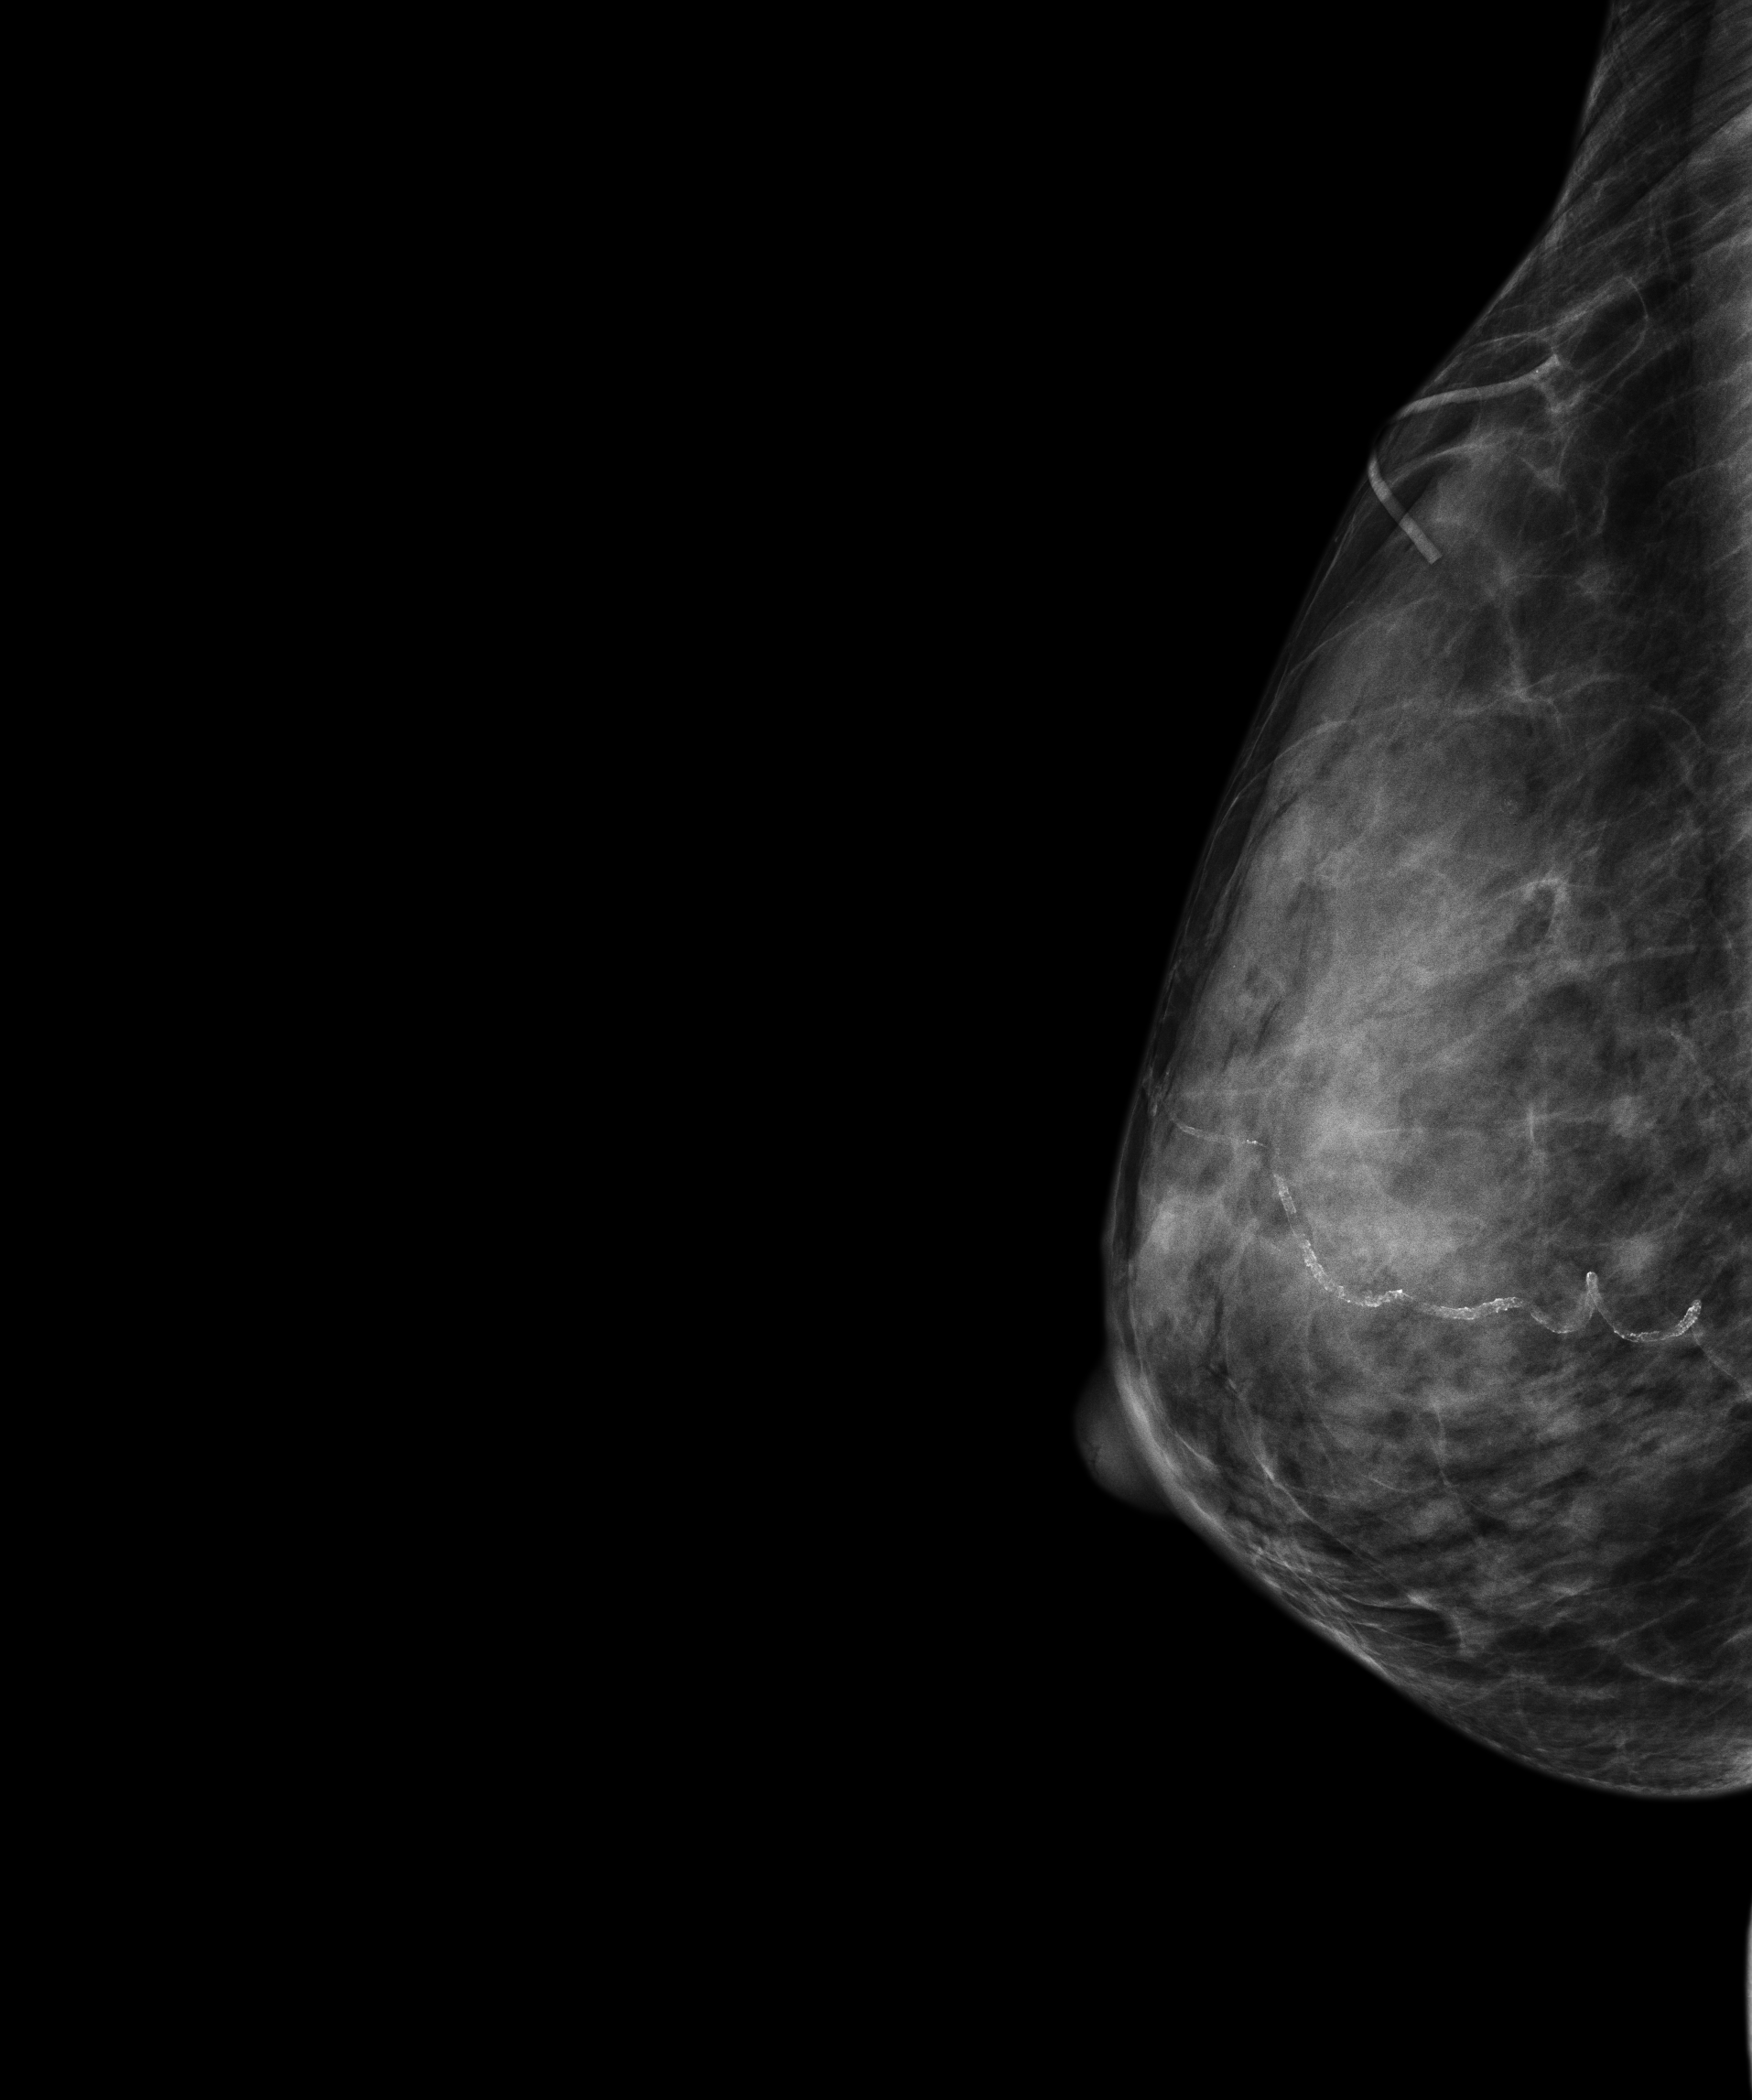
Annual screening mammography examination; compressed breast thickness 29 mm. Patient: female, 60 years.
Image type: full-field digital mammogram. Breast: right. Projection: laterally exaggerated craniocaudal (XCCL) view.